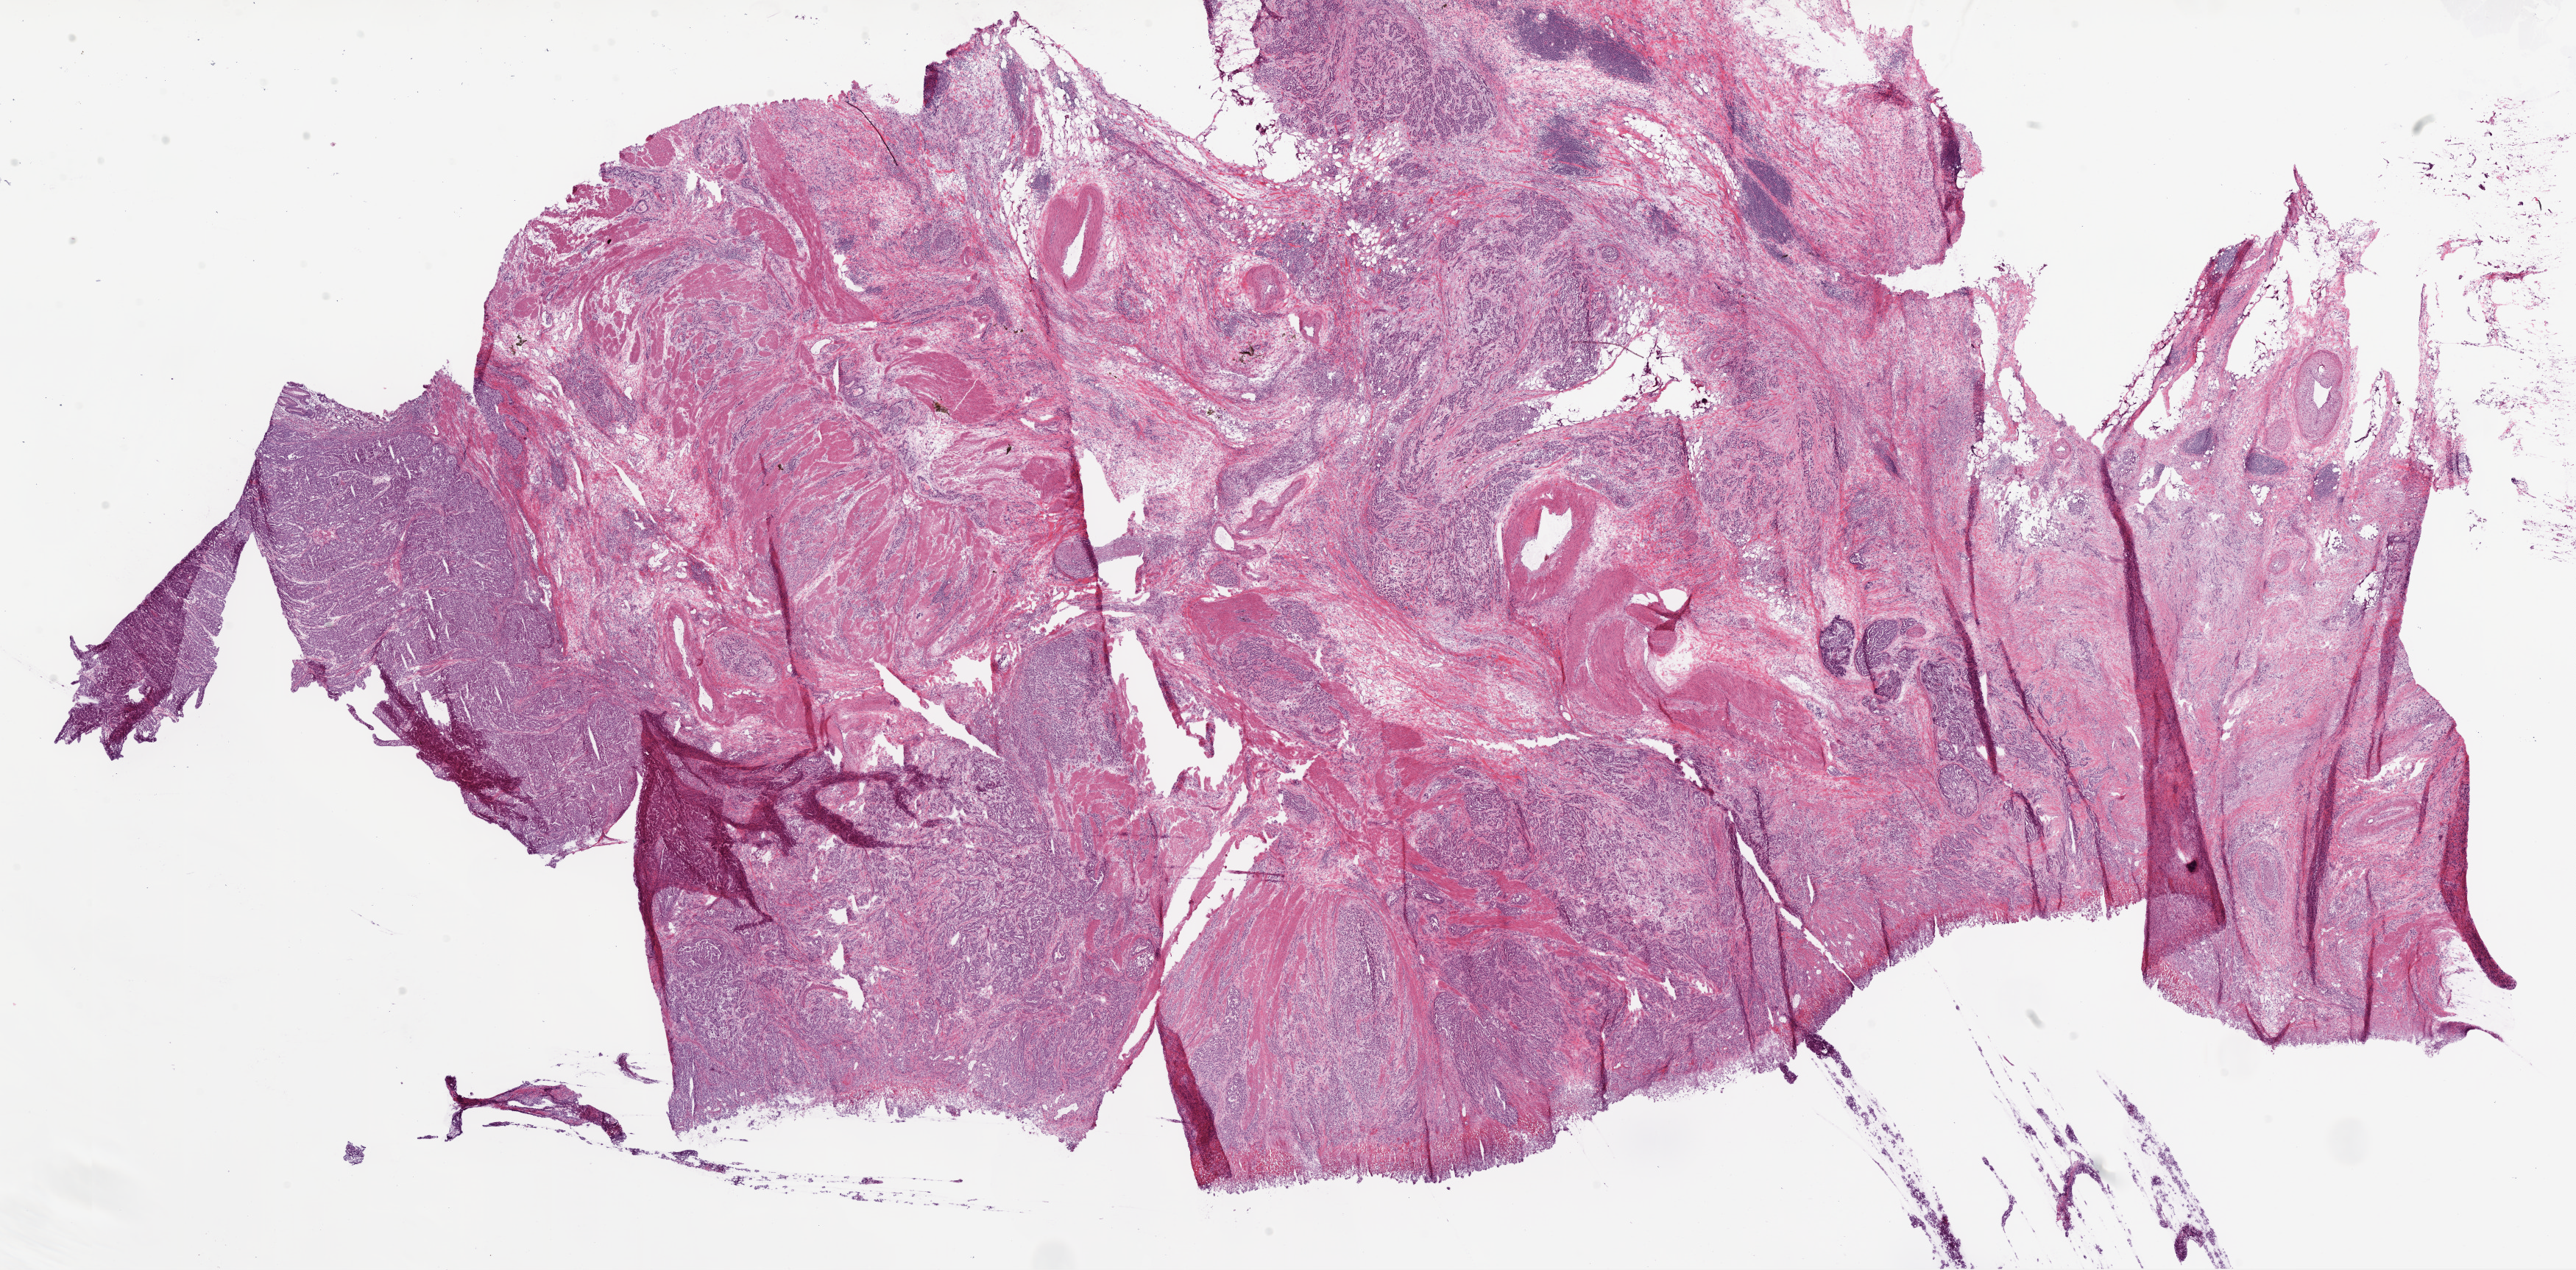
Digitized H&E-stained tissue section (whole slide), whole scanned area (about 28.1 x 13.8 mm) shown as a low-resolution overview; frozen section from the bottom of the tissue portion; sample: primary tumour, stomach. Female, age 55 years at initial diagnosis. Histologic grade: G3 (poorly differentiated). Slide review estimates, as recorded: tumour cells 60%, tumour nuclei 75%, normal cells 0%, stromal cells 40%, necrosis 0%.
Pathologic diagnosis: Adenocarcinoma, NOS (cardia, NOS). AJCC pathologic stage: IIIA (6th edition).